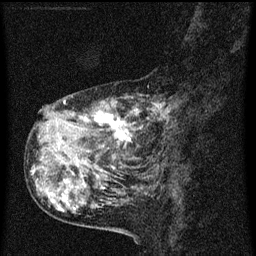
Breast MRI (dynamic contrast-enhanced), one sagittal slice. Position 18 of 60 along the scan axis. Dynamic contrast-enhanced series, image 2 of 3 at this slice position (ordered by acquisition). 1.5 T. TE 4.2 ms, TR 8 ms. 256 × 256 image matrix, field of view 180 × 180 mm. Female patient, age 55 years.
Annotated regions visible in this slice (semi-automatically segmented with operator editing):
- analysis volume of interest (the breast-tissue region the enhancement analysis was run in; not a lesion): bounding box [x1, y1, x2, y2] px = [38, 92, 177, 159]
- tumour enhancement mask (voxels above the 70 % enhancement threshold inside the analysis volume of interest): [64, 100, 171, 143]